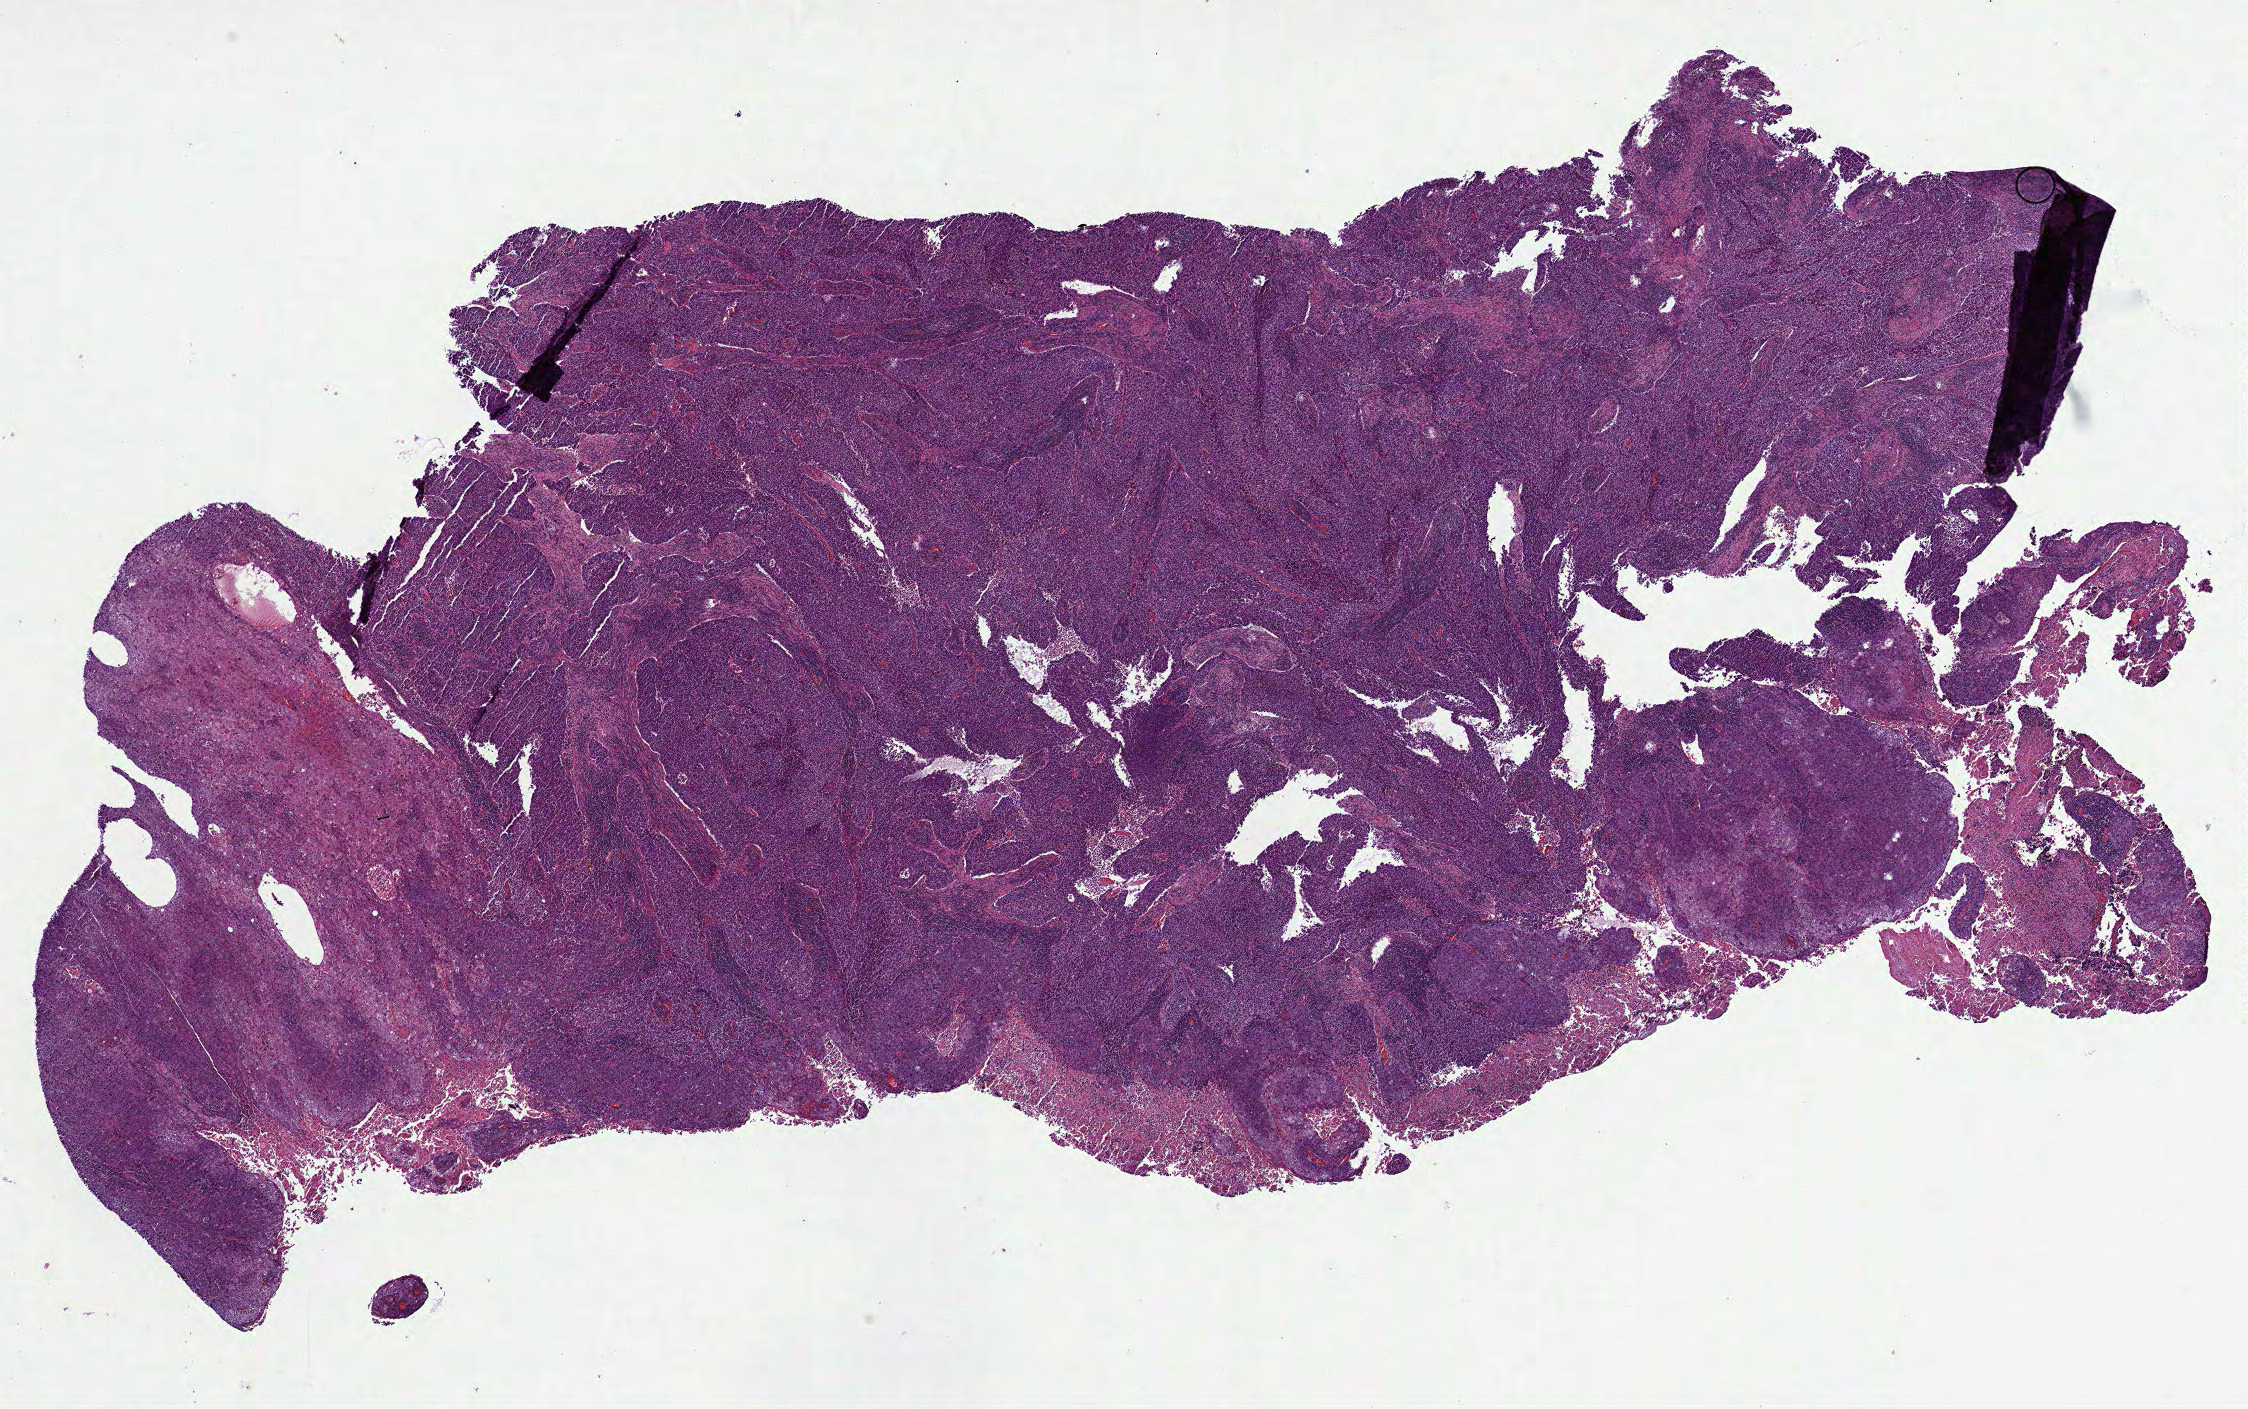
Hematoxylin and eosin (H&E) stained whole-slide image — whole scanned area (about 18.1 x 11.4 mm, slide scanned at 40x) shown as a low-resolution overview; formalin-fixed paraffin-embedded (FFPE) diagnostic section; bladder, primary tumour sample. Patient sex: female. Histologic grade: high grade.
* pathologic diagnosis: Transitional cell carcinoma
* AJCC pathologic stage: IV